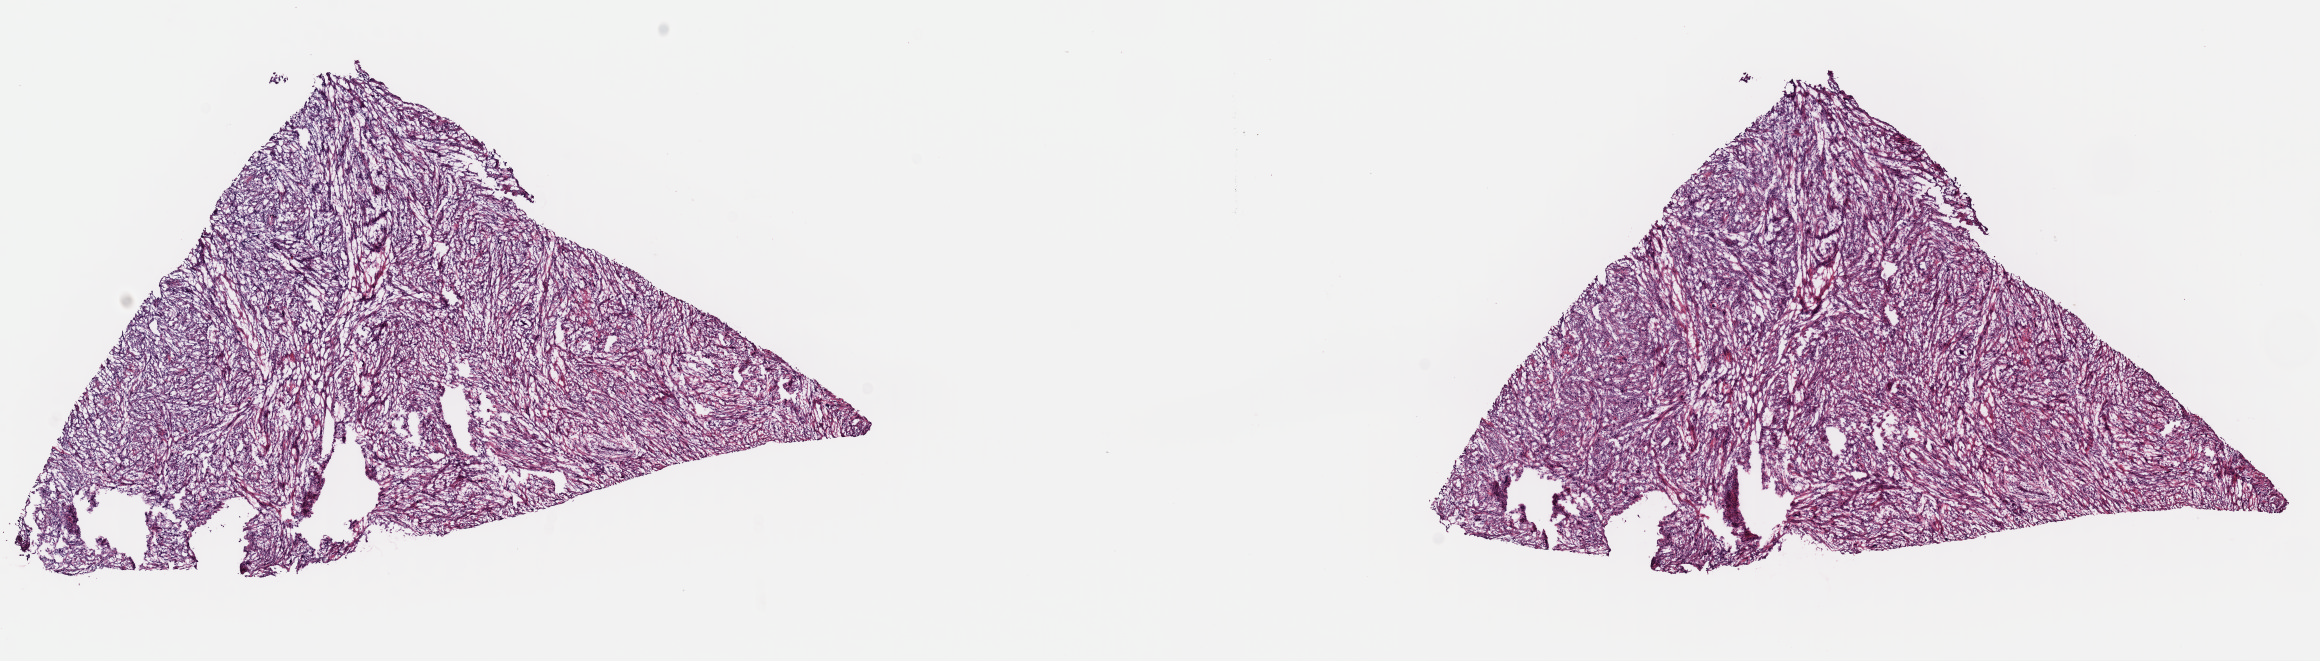
H&E whole-slide image — low-resolution overview of the scanned area, about 18.3 x 5.2 mm; frozen section from the top of the tissue portion; retroperitoneum and peritoneum, primary tumour sample. Male patient; age at initial diagnosis 53 years. Slide review estimates, as recorded: tumour cells 95%, tumour nuclei 95%, normal cells 0%, stromal cells 5%, necrosis 0%. Infiltration values recorded for this section: lymphocyte infiltration 0%, monocyte infiltration 0%, neutrophil infiltration 0%.
Pathologic diagnosis: Dedifferentiated liposarcoma (retroperitoneum).